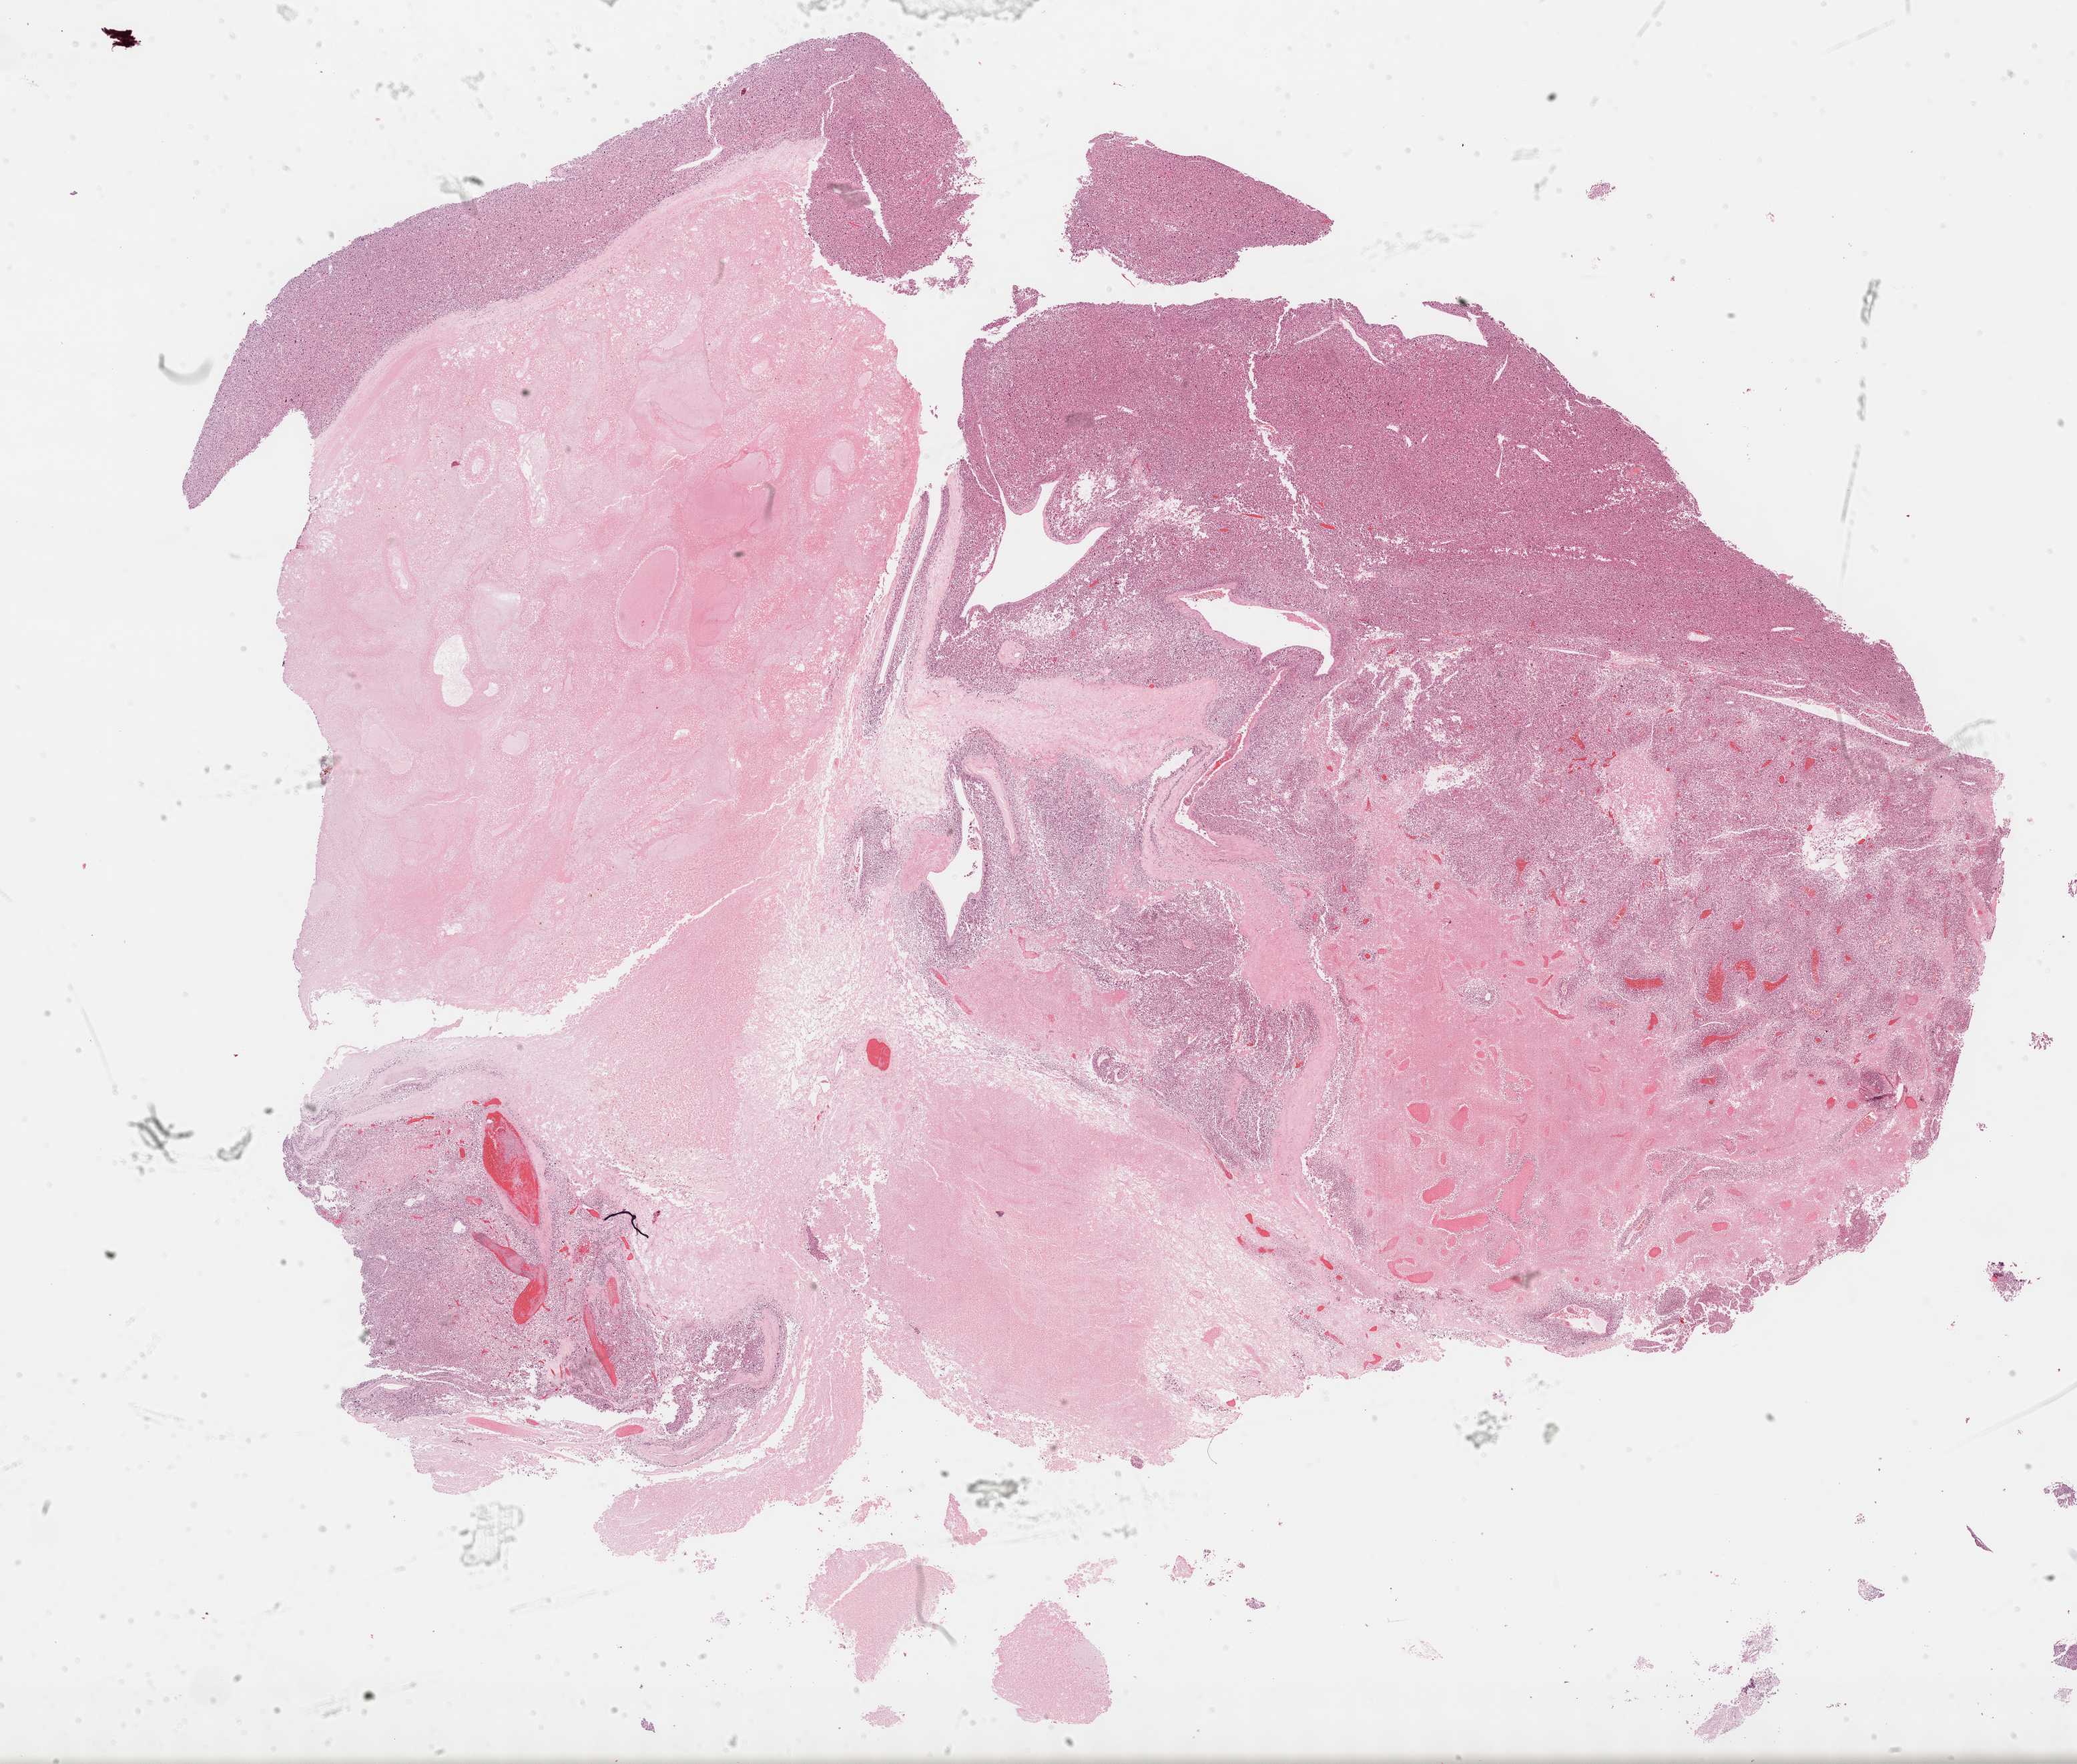
Digitized Hematoxylin and eosin (H&E) stained tissue section (whole slide), low-resolution overview of the scanned area, about 25.2 x 21.4 mm (acquisition: 40x scan), formalin-fixed paraffin-embedded (FFPE) diagnostic section, primary tumour sample from the adrenal cortex. Female patient; age at initial diagnosis 64 years.
* diagnosis: Adrenal cortical carcinoma (cortex of adrenal gland)